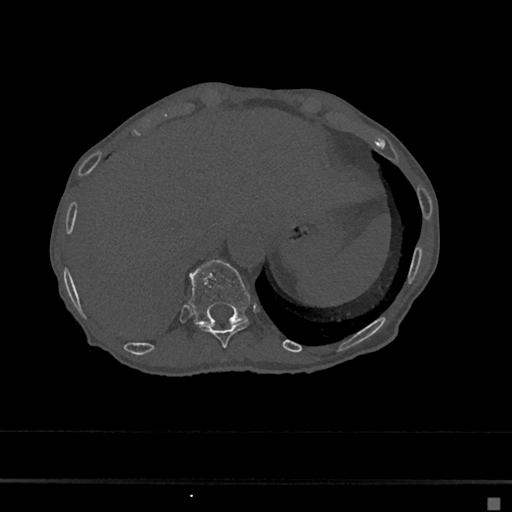
CT including the spine, one axial slice. Slice 198 of 797 in the series (ordered by position). Bone window (W 1800 / L 400 HU). 512 × 512 image matrix, field of view 360 × 360 mm. Patient: female, 68 years. Case-level facts recorded for this patient, not image findings: primary cancer: renal.
Annotated regions visible in this slice (semi-automatic segmentation, software-assisted and operator-edited):
- T10 vertebra: bounding box (x1, y1, x2, y2) in pixels: (196, 321, 249, 348)
- T11 vertebra: (189, 259, 251, 325)